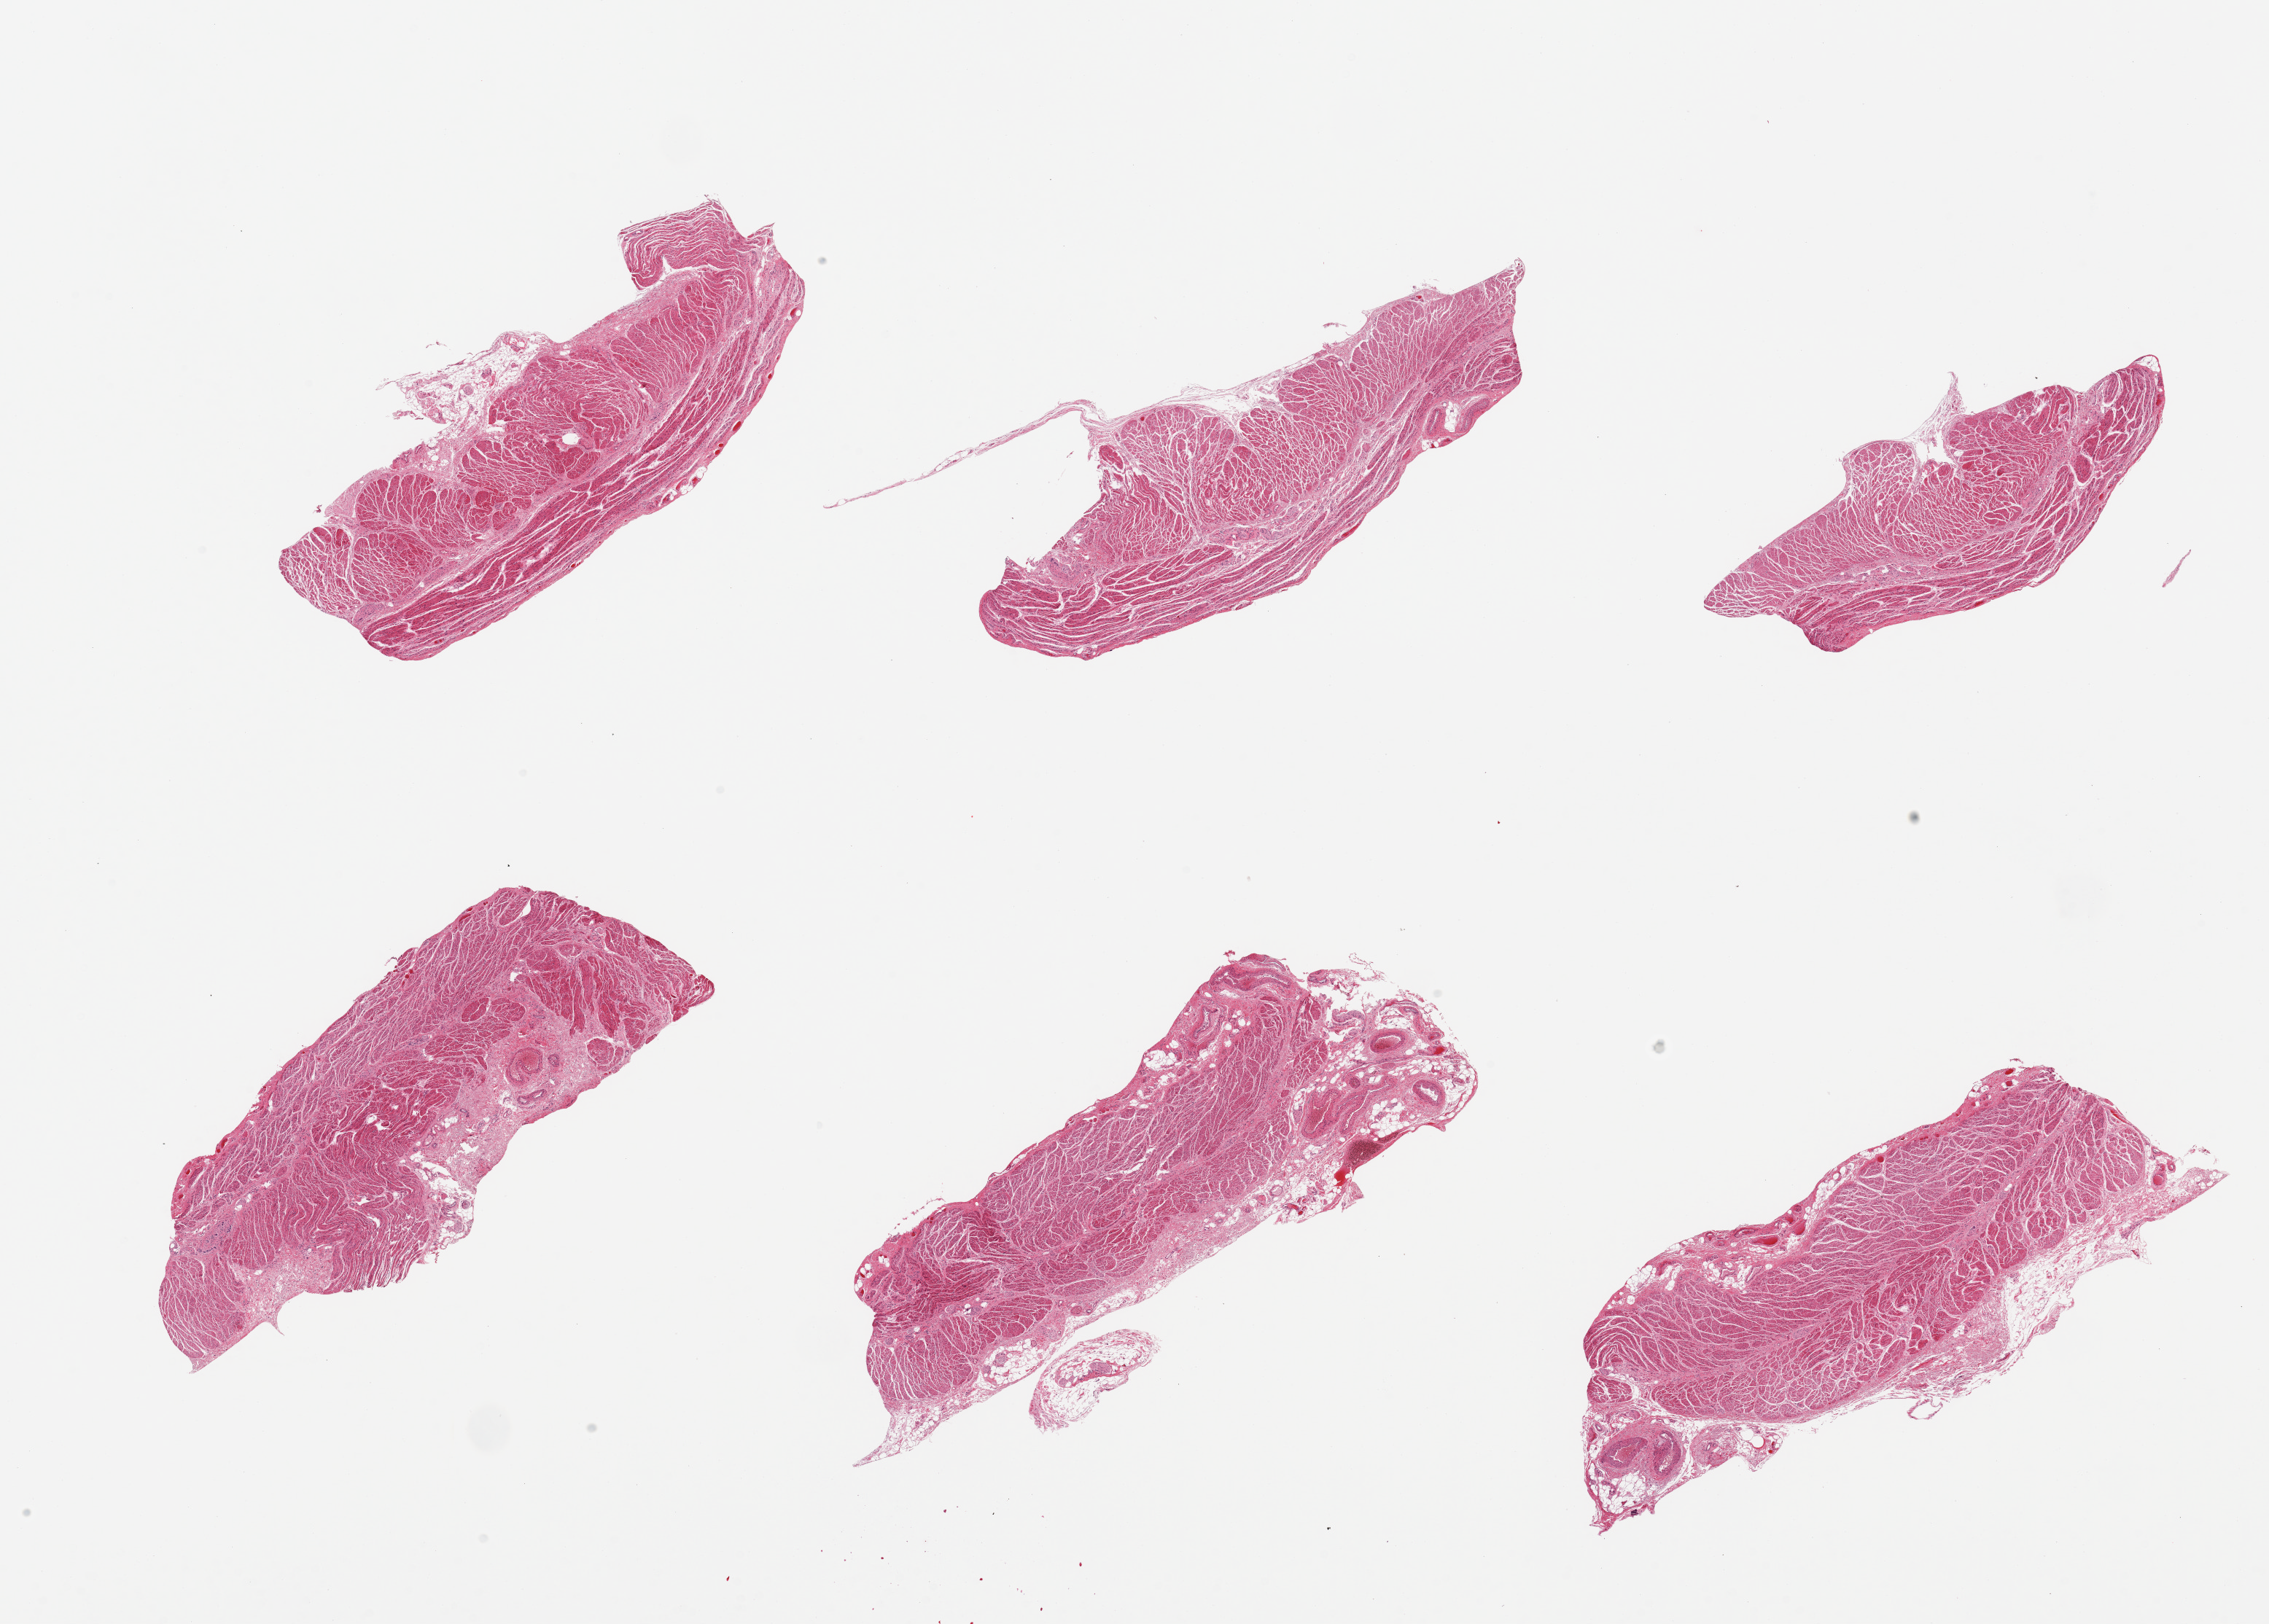
Digitized H&E-stained section — shown as a low-resolution overview of the whole scanned area (about 24.6 x 17.6 mm, from a 20x scan); PAXgene-fixed paraffin-embedded (PFPE) section; target tissue: gastroesophageal junction; donor tissue sample. Donor: female.
* pathologist's review note for this sample: 6 pieces; well dissected